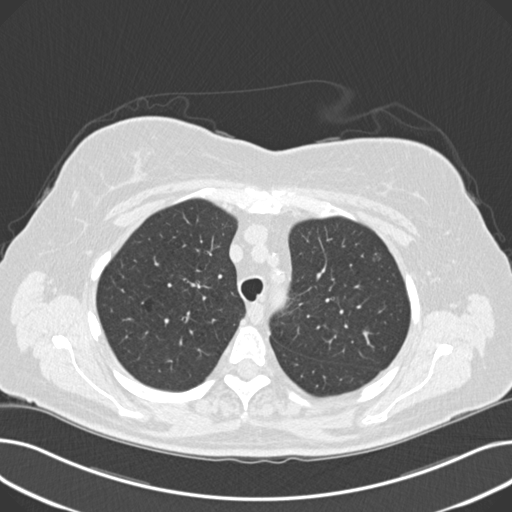
Axial slice from a low-dose chest CT screening exam; third annual screen; lung window (W 1500 / L -600 HU); 120 kVp. Female participant, aged 60 years at enrolment. Current smoker at enrolment.
Expert-annotated lung lesion, bounding box <360,240,397,276> (left, top, right, bottom; pixels). The screening reader recorded 8 non-calcified nodules or masses ≥4 mm on this exam; which of them this box marks is not recorded.